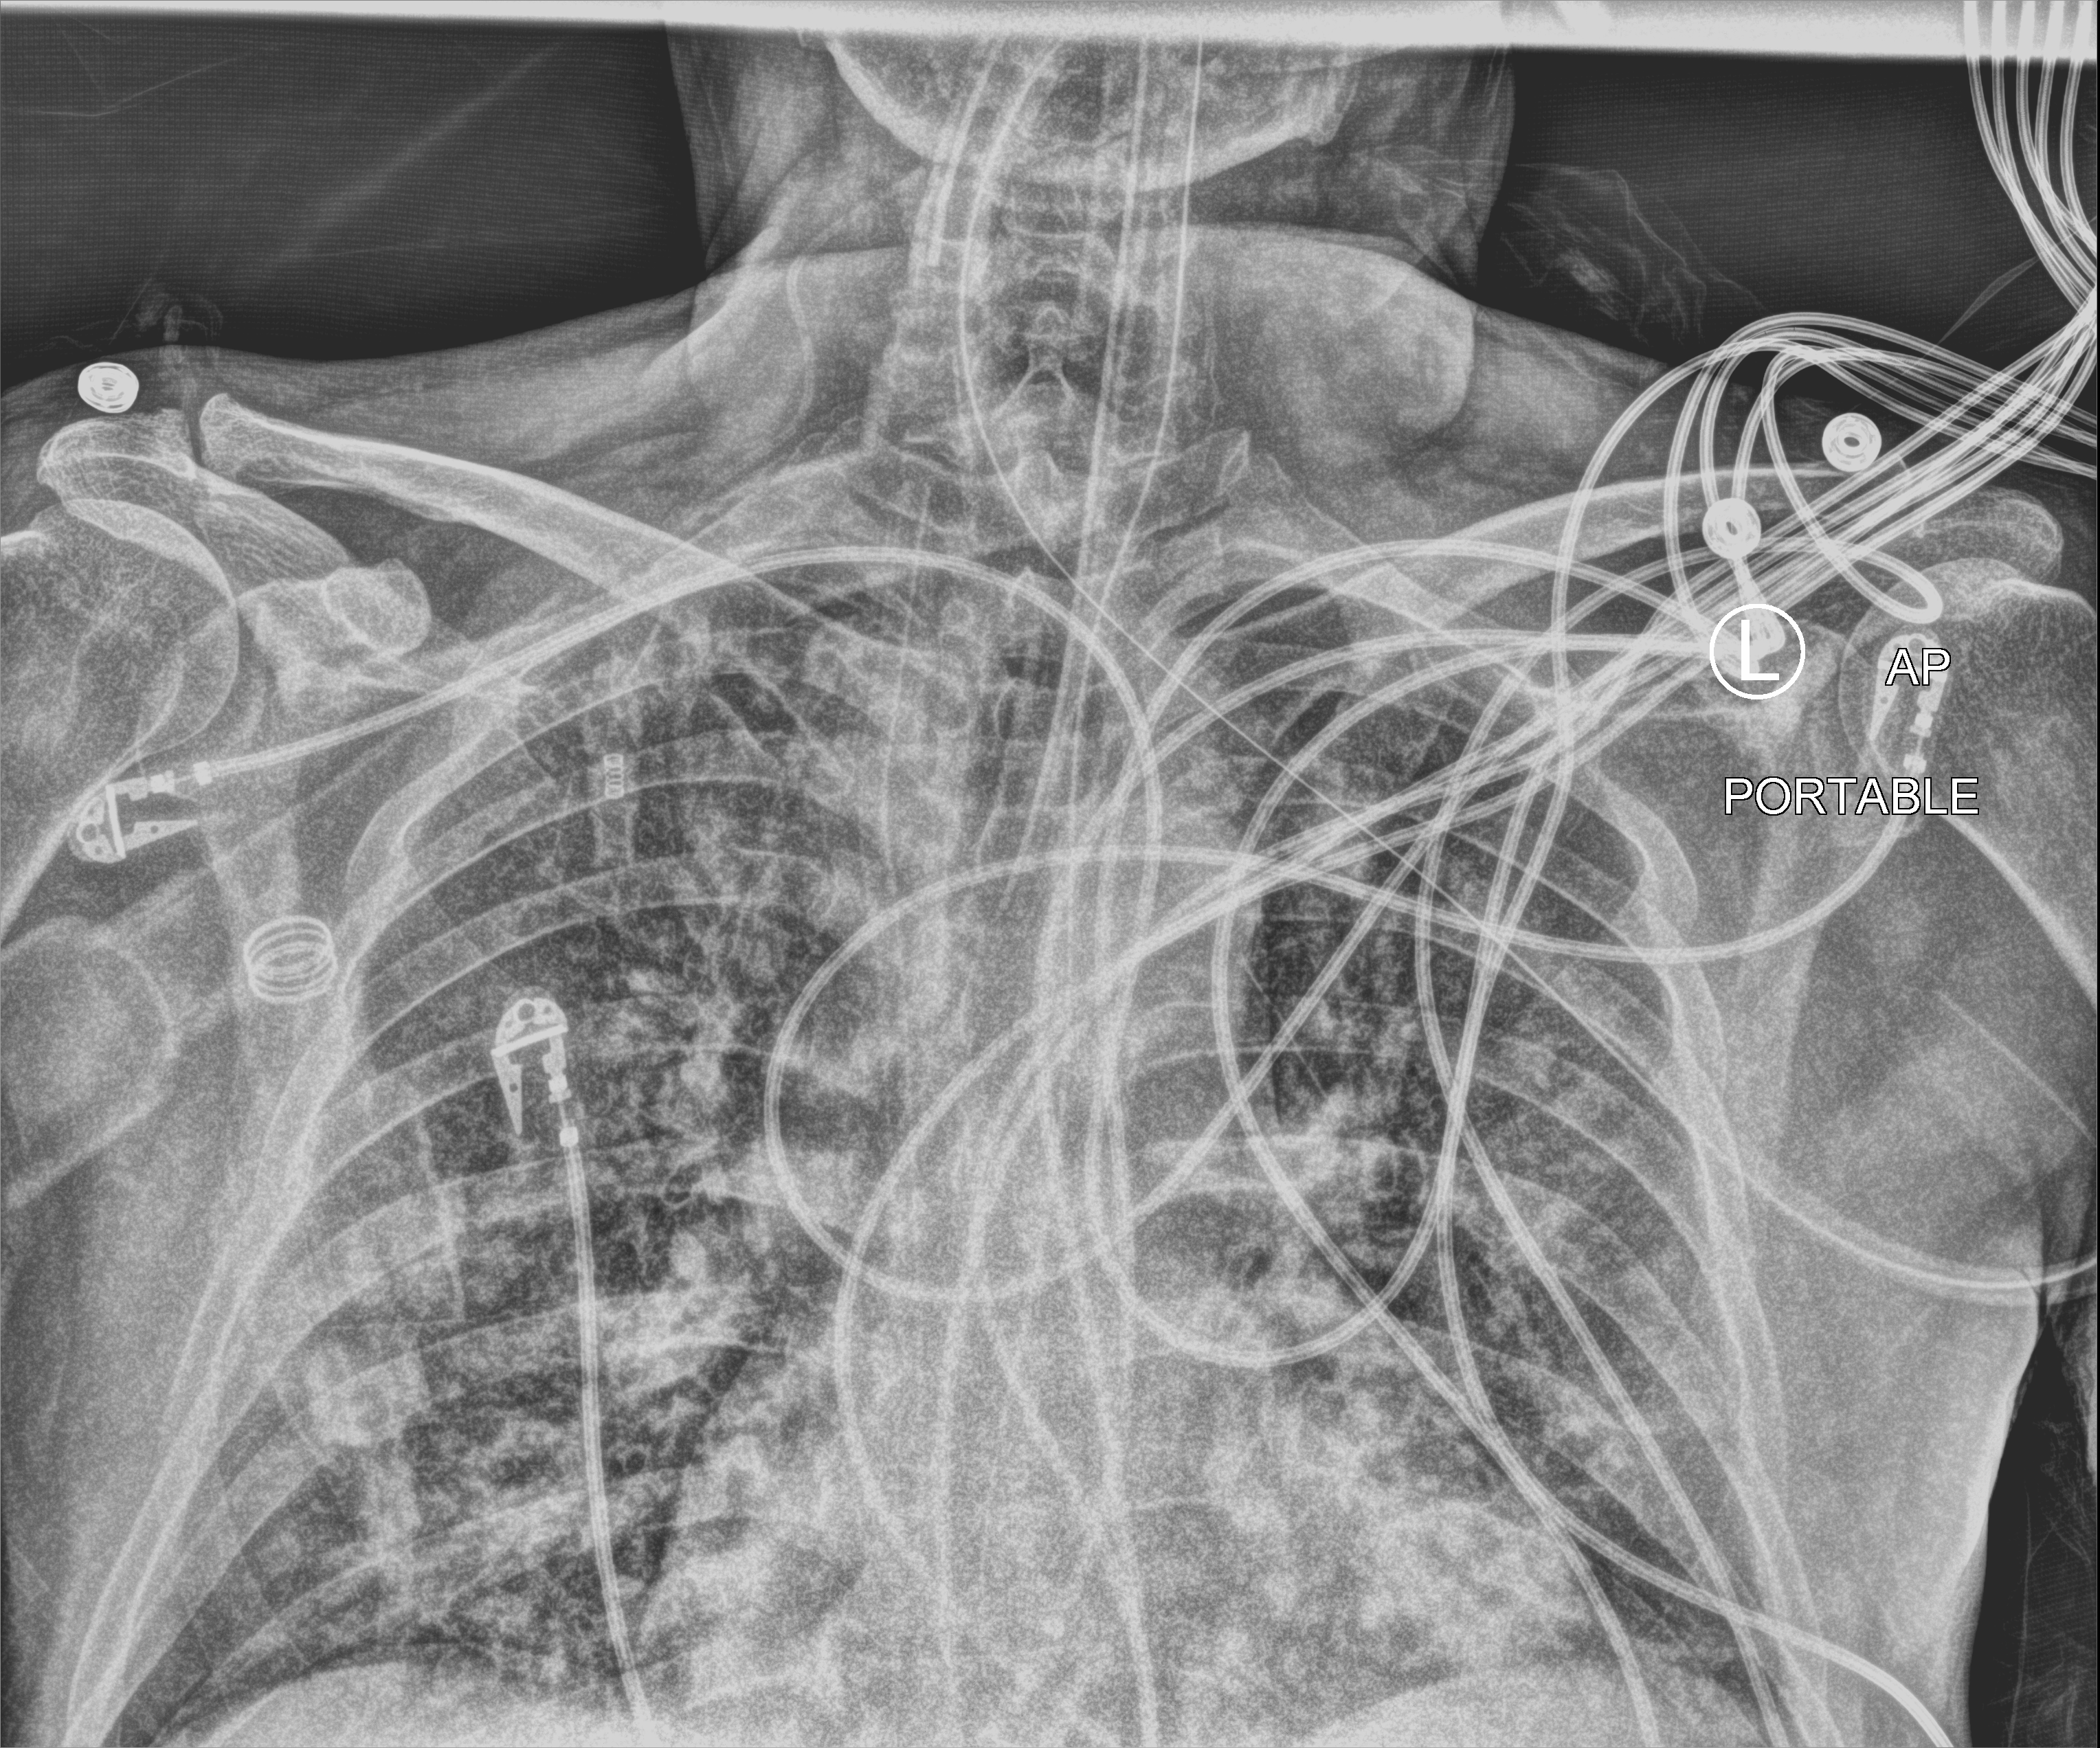
Chest X-ray (portable); anteroposterior (AP) projection. Male patient hospitalised with COVID-19, age 18–59 years.
Hospital-stay facts (about this admission, not read from this image; timing relative to this image not recorded): mechanically ventilated during this hospital stay: yes; hypertension (admission record): no; length of hospital stay: 19 days.